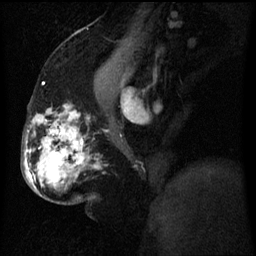
Breast MRI (dynamic contrast-enhanced), one sagittal slice; slice 32 of 60 in the series (ordered by position); dynamic contrast-enhanced series, image 2 of 3 at this slice position (ordered by acquisition); 1.5 T; TE 4.2 ms, TR 8 ms; 2.5 mm slice thickness; 256 × 256 image matrix, field of view 200 × 200 mm. Patient: female, 50 years.
Annotated regions visible in this slice (semi-automatically segmented with operator editing):
- analysis volume of interest (the breast-tissue region the enhancement analysis was run in; not a lesion): bounding box [x1, y1, x2, y2] px = [25, 128, 85, 197]
- tumour enhancement mask (voxels above the 70 % enhancement threshold inside the analysis volume of interest): [26, 130, 81, 181]